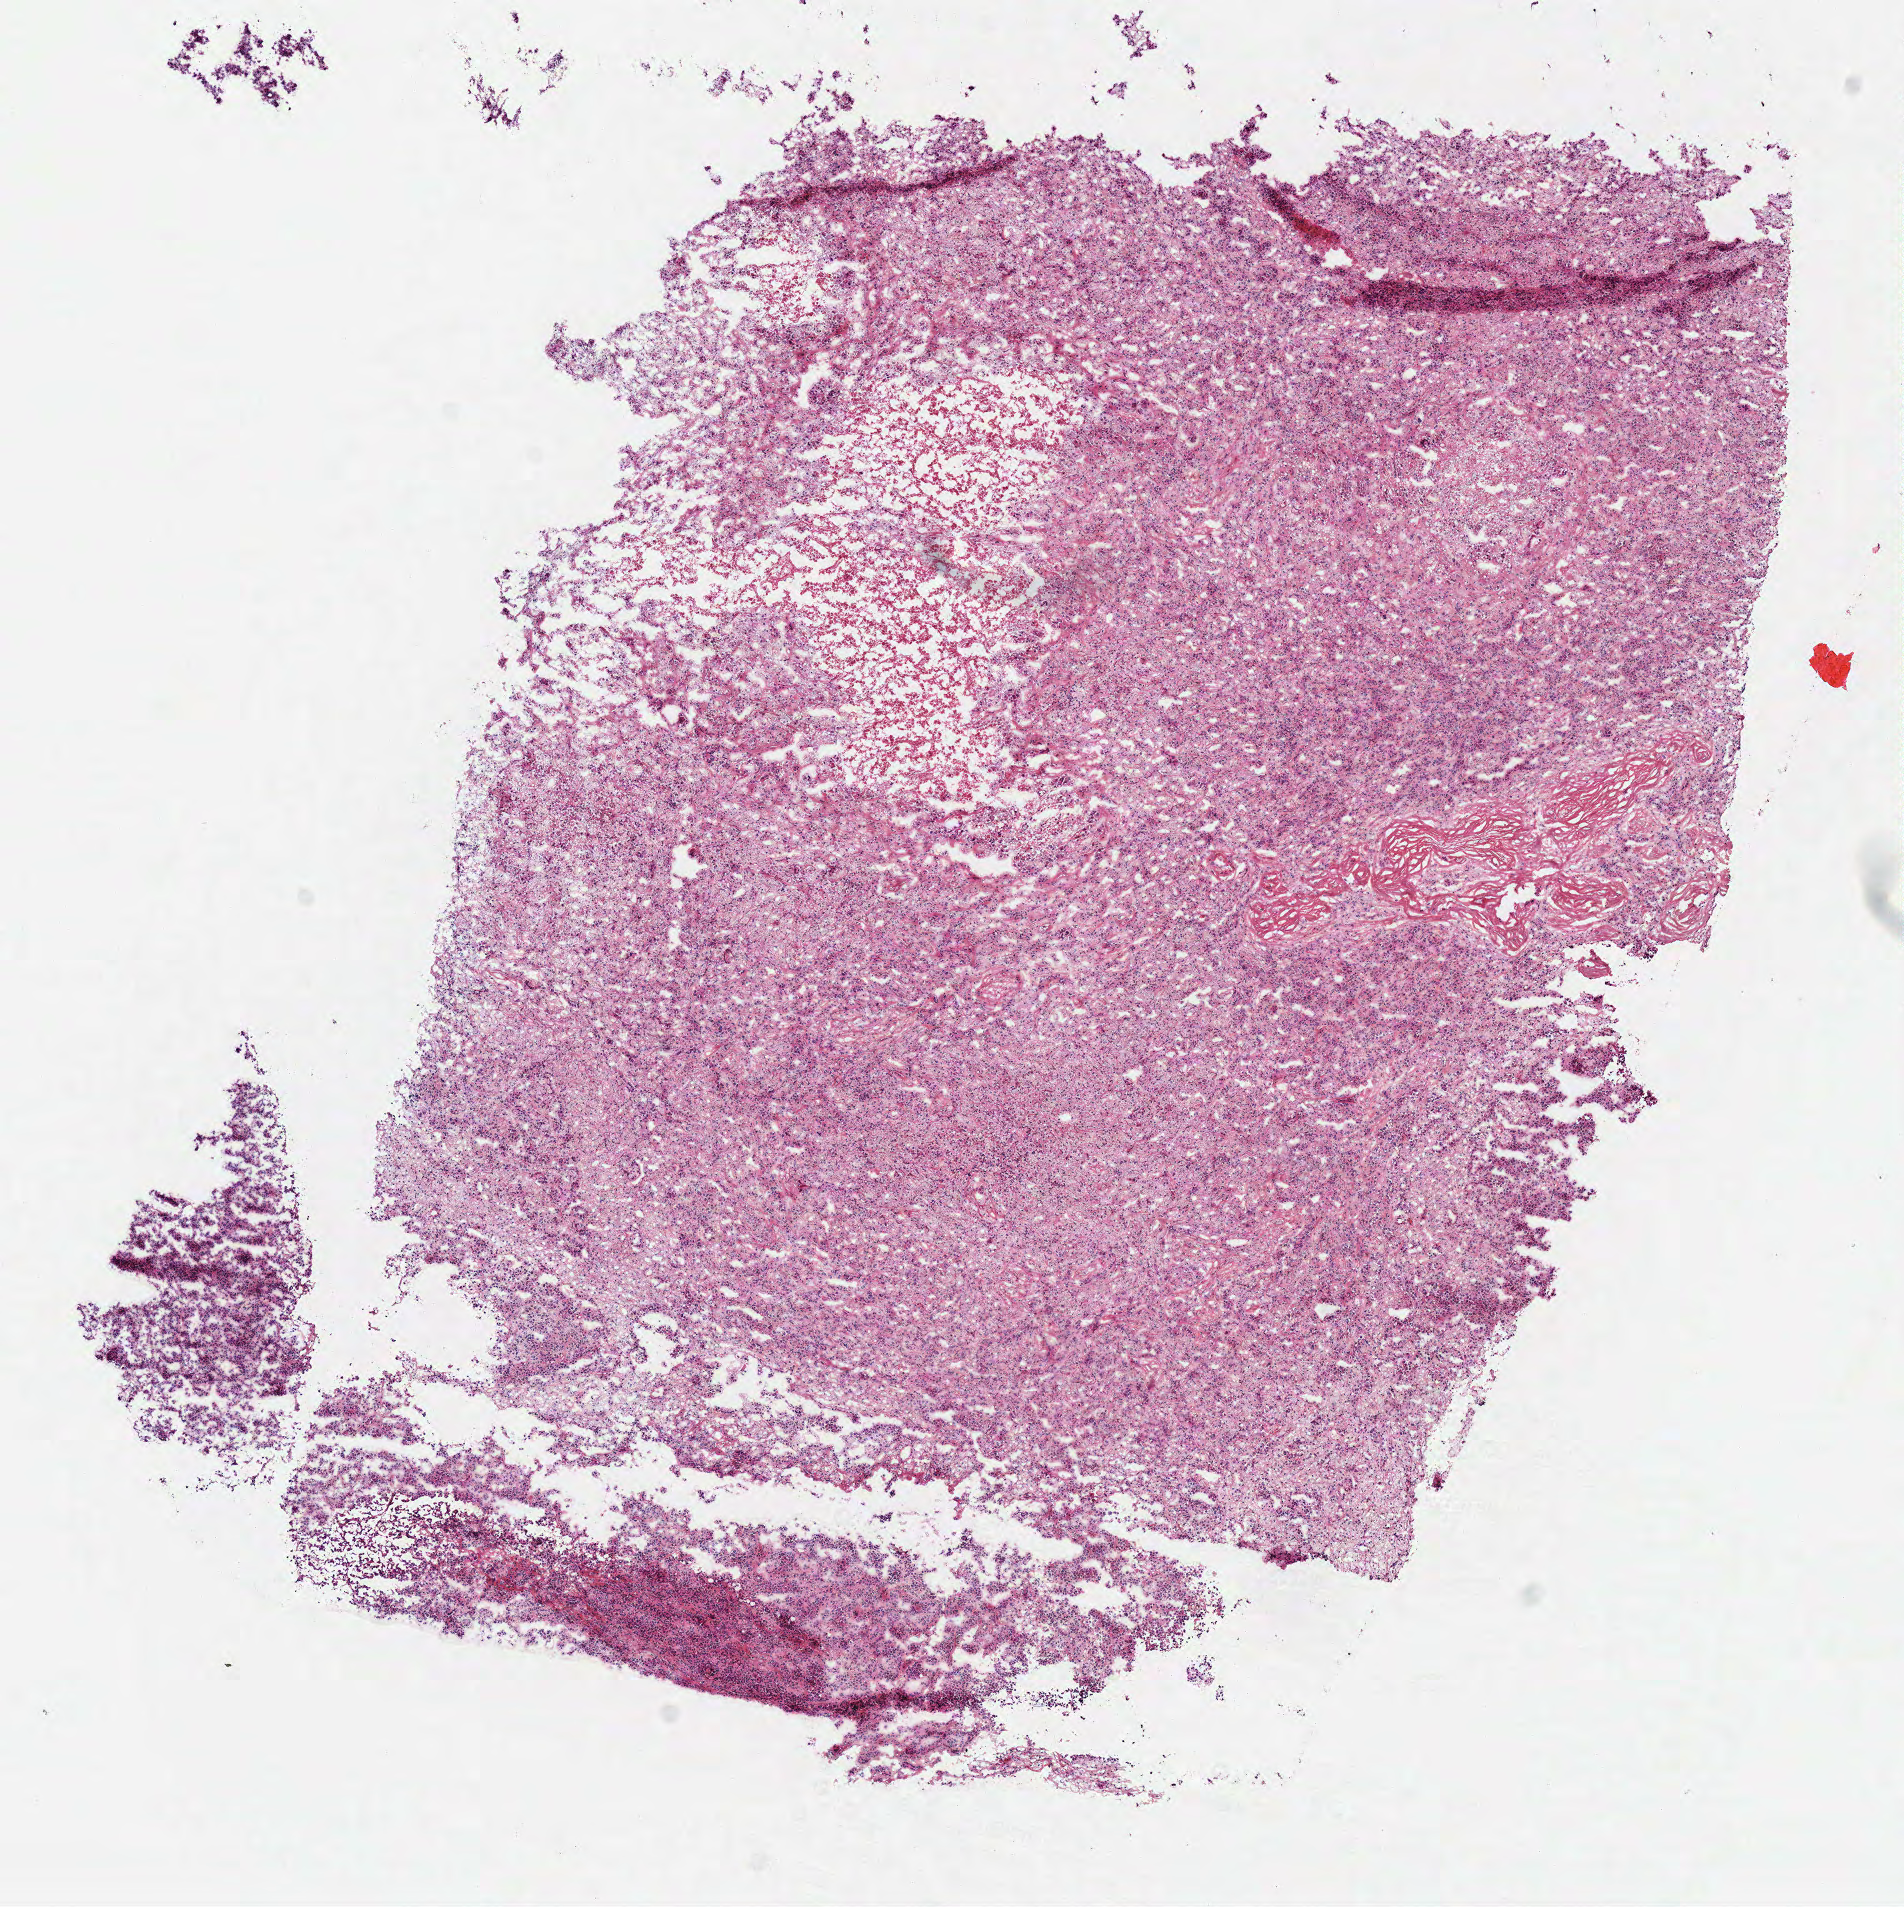
Digitized Hematoxylin and eosin (H&E) stained tissue section (whole slide), shown as a low-resolution overview of the whole scanned area (about 7.5 x 7.5 mm, slide scanned at 40x). Frozen section. Primary tumour sample from the kidney. Male patient; age at initial diagnosis 69 years. Pathologist review of this section (percent, as recorded): tumour cells 78%, tumour nuclei 75%, normal cells 0%, stromal cells 10%, necrosis 12%.
AJCC pathologic stage: I. Pathologic diagnosis: Papillary adenocarcinoma, NOS.